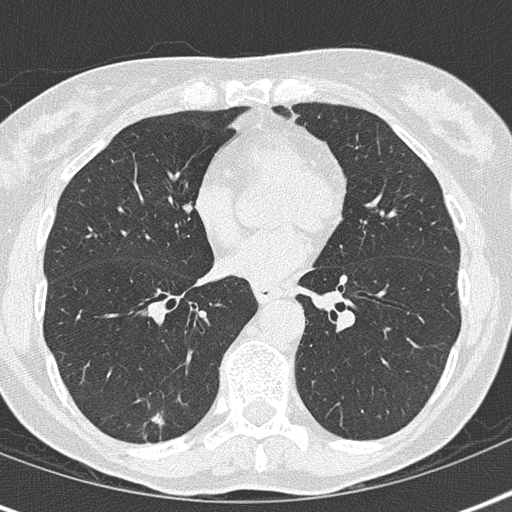
Chest CT (low-dose screening protocol), one axial image, baseline screening round, lung window (W 1500 / L -600 HU). Female participant, aged 69 years at enrolment. Current smoker at enrolment.
• Expert reader's lesion annotation, bounding box (x1, y1, x2, y2) in pixels: (119, 388, 182, 449).
• The screening reader recorded 2 non-calcified nodules or masses ≥4 mm on this exam (right lower lobe, left lower lobe); which of them this box marks is not recorded.